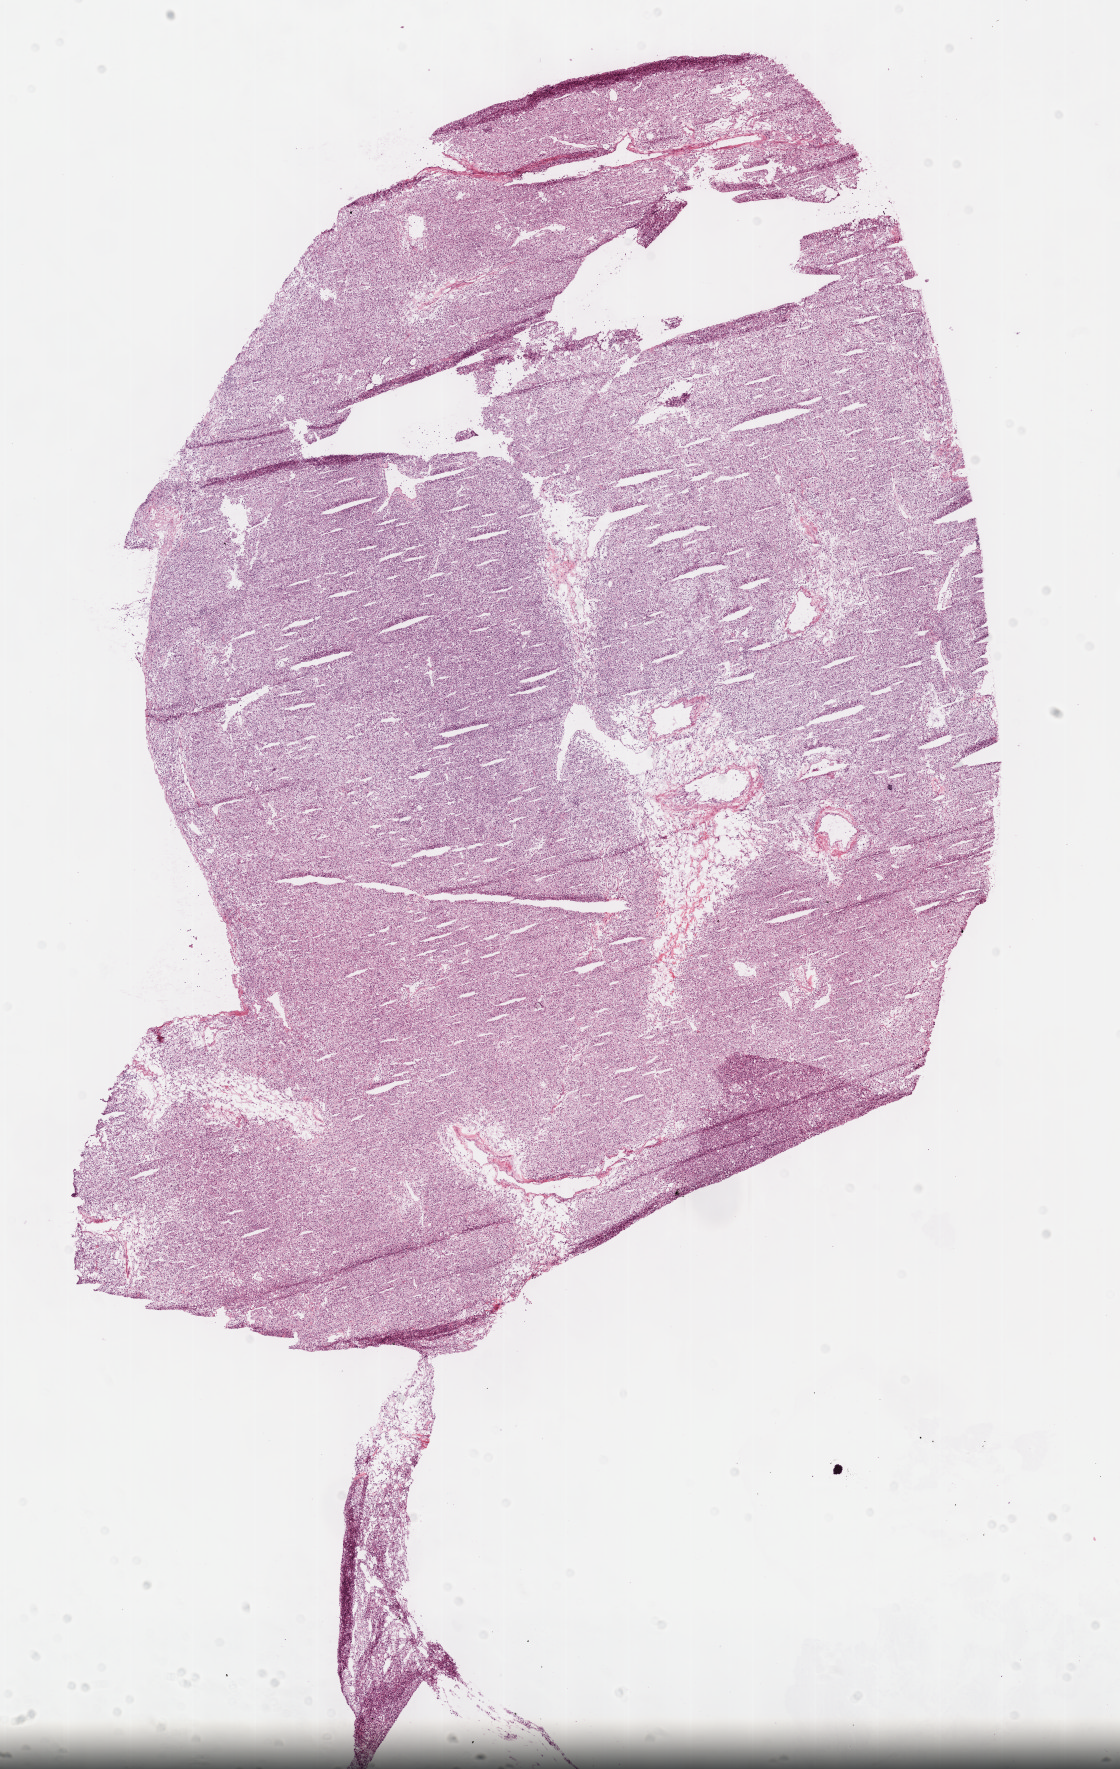
Hematoxylin and eosin (H&E) stained whole-slide image, a low-resolution overview of the entire scanned area, about 9.1 x 14.3 mm (acquisition: 40x scan), frozen section from the top of the tissue portion, sample: primary tumour, kidney. Patient: male, age at initial diagnosis 74 years. Histologic grade: G2 (moderately differentiated). Slide review estimates, as recorded: tumour cells 95%, tumour nuclei 85%, normal cells 0%, stromal cells 5%, necrosis 0%.
Histologic diagnosis: Clear cell adenocarcinoma, NOS. AJCC pathologic stage: I. TNM: T1a NX M0.